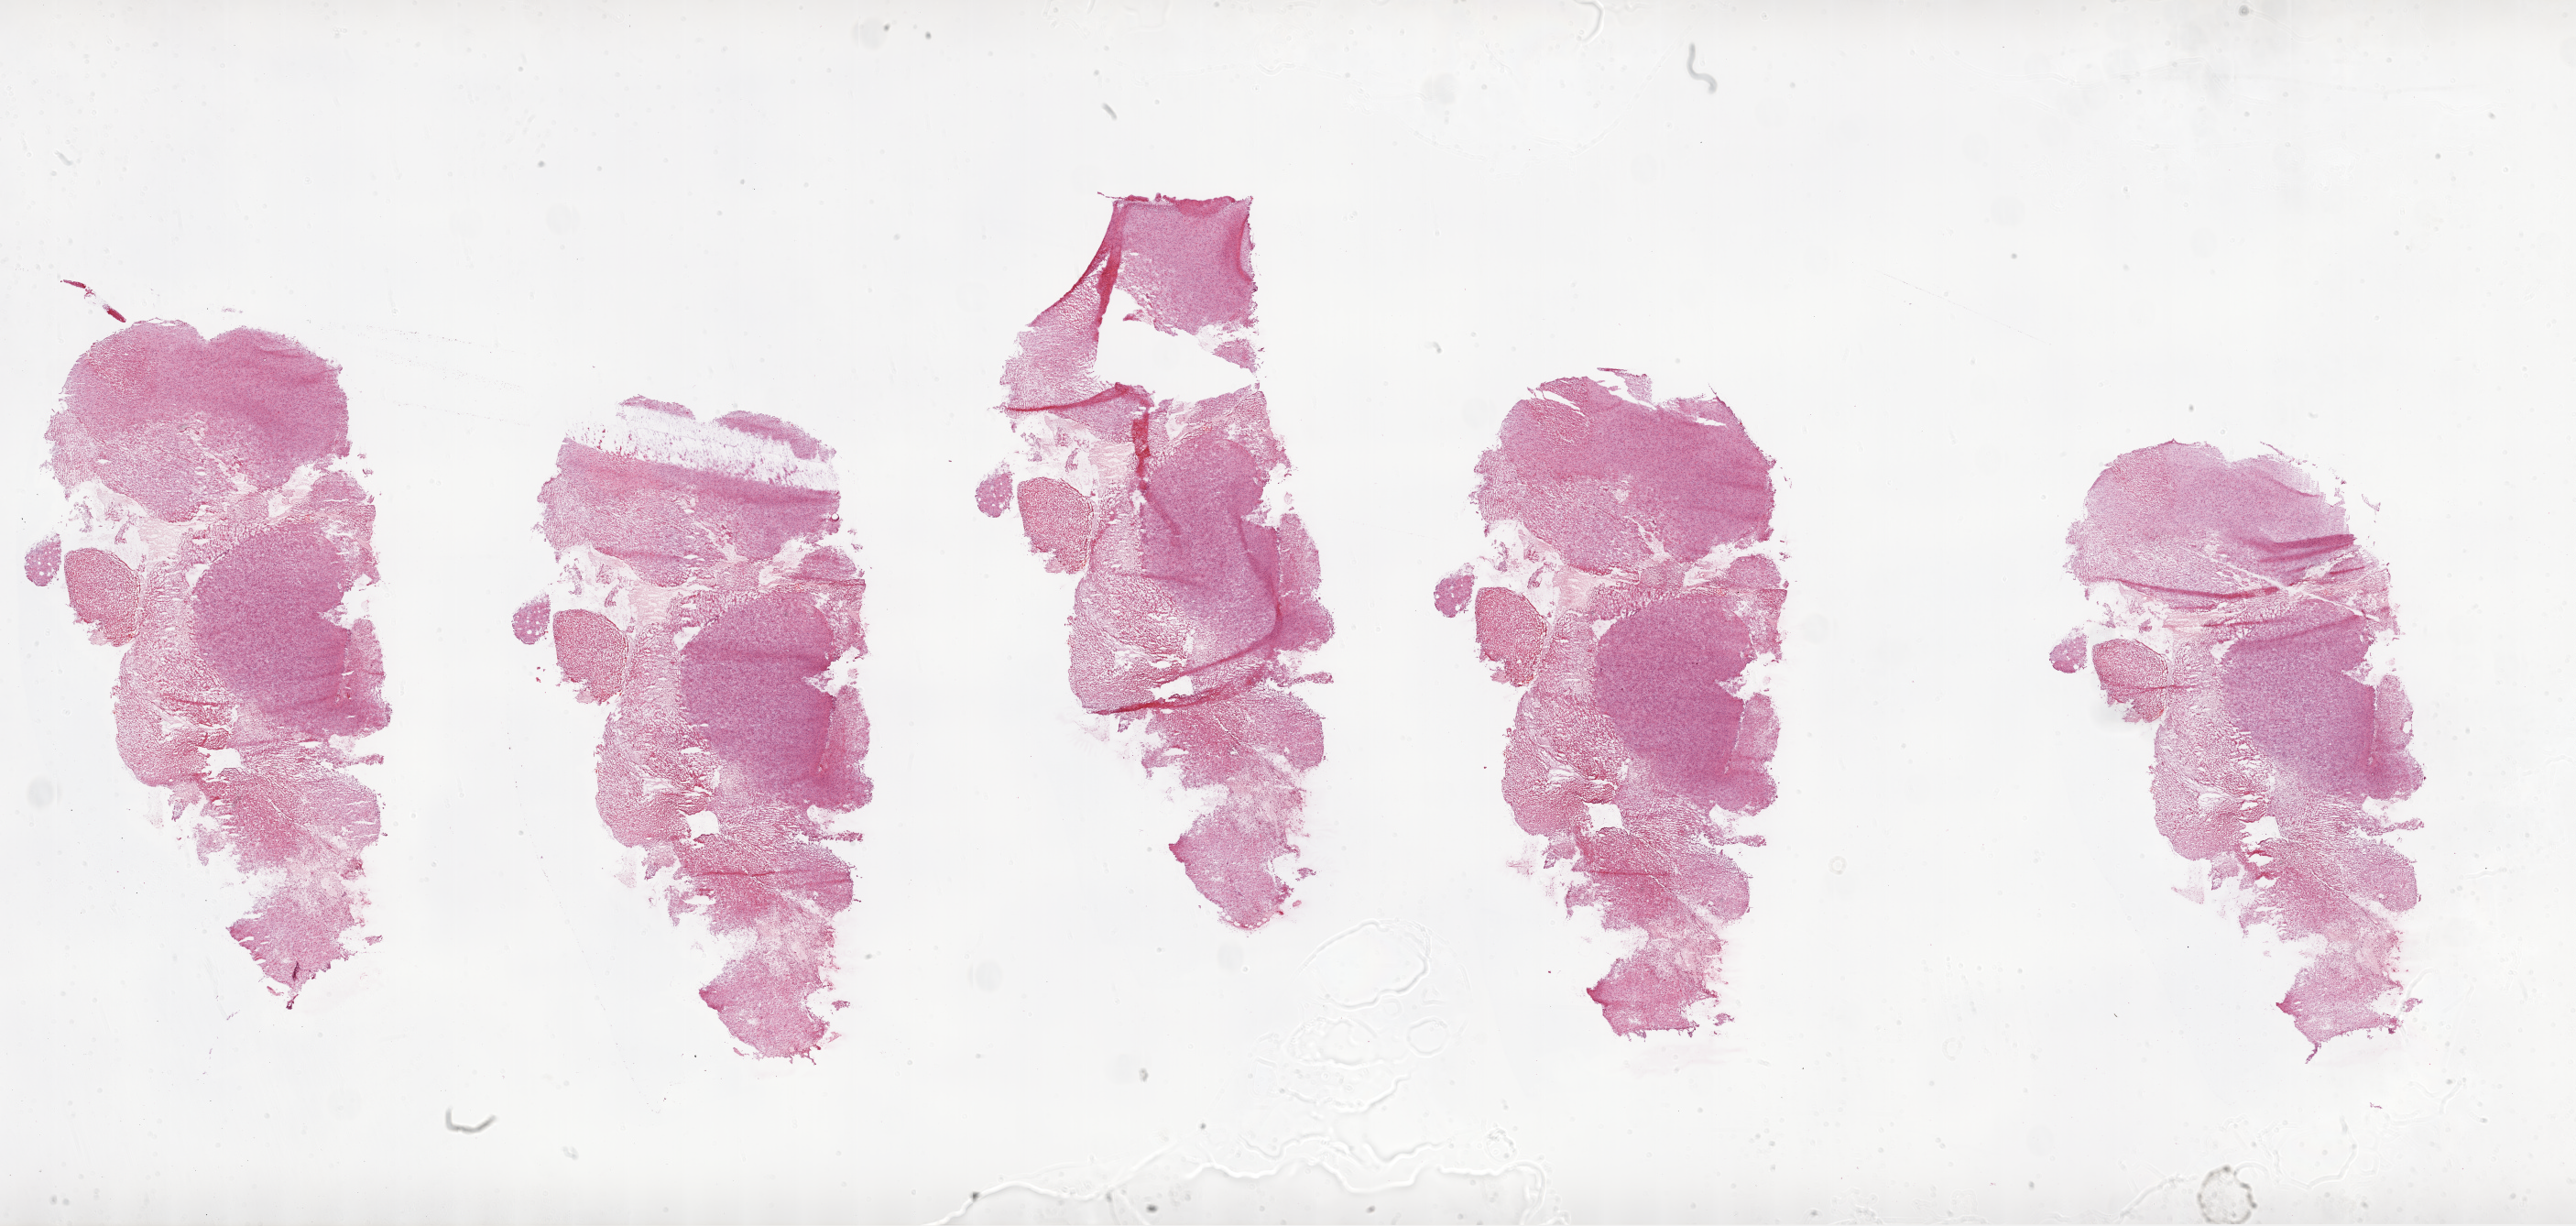
H&E-stained whole-slide image — shown as a low-resolution overview of the whole scanned area (about 45.1 x 21.5 mm). Frozen section. Sample: primary tumour, brain. Patient: male, age at initial diagnosis 56 years. Pathologist review of this section (percent, as recorded): tumour cells 65%, tumour nuclei 85%, normal cells 10%, stromal cells 10%, necrosis 15%.
• diagnosis: Glioblastoma